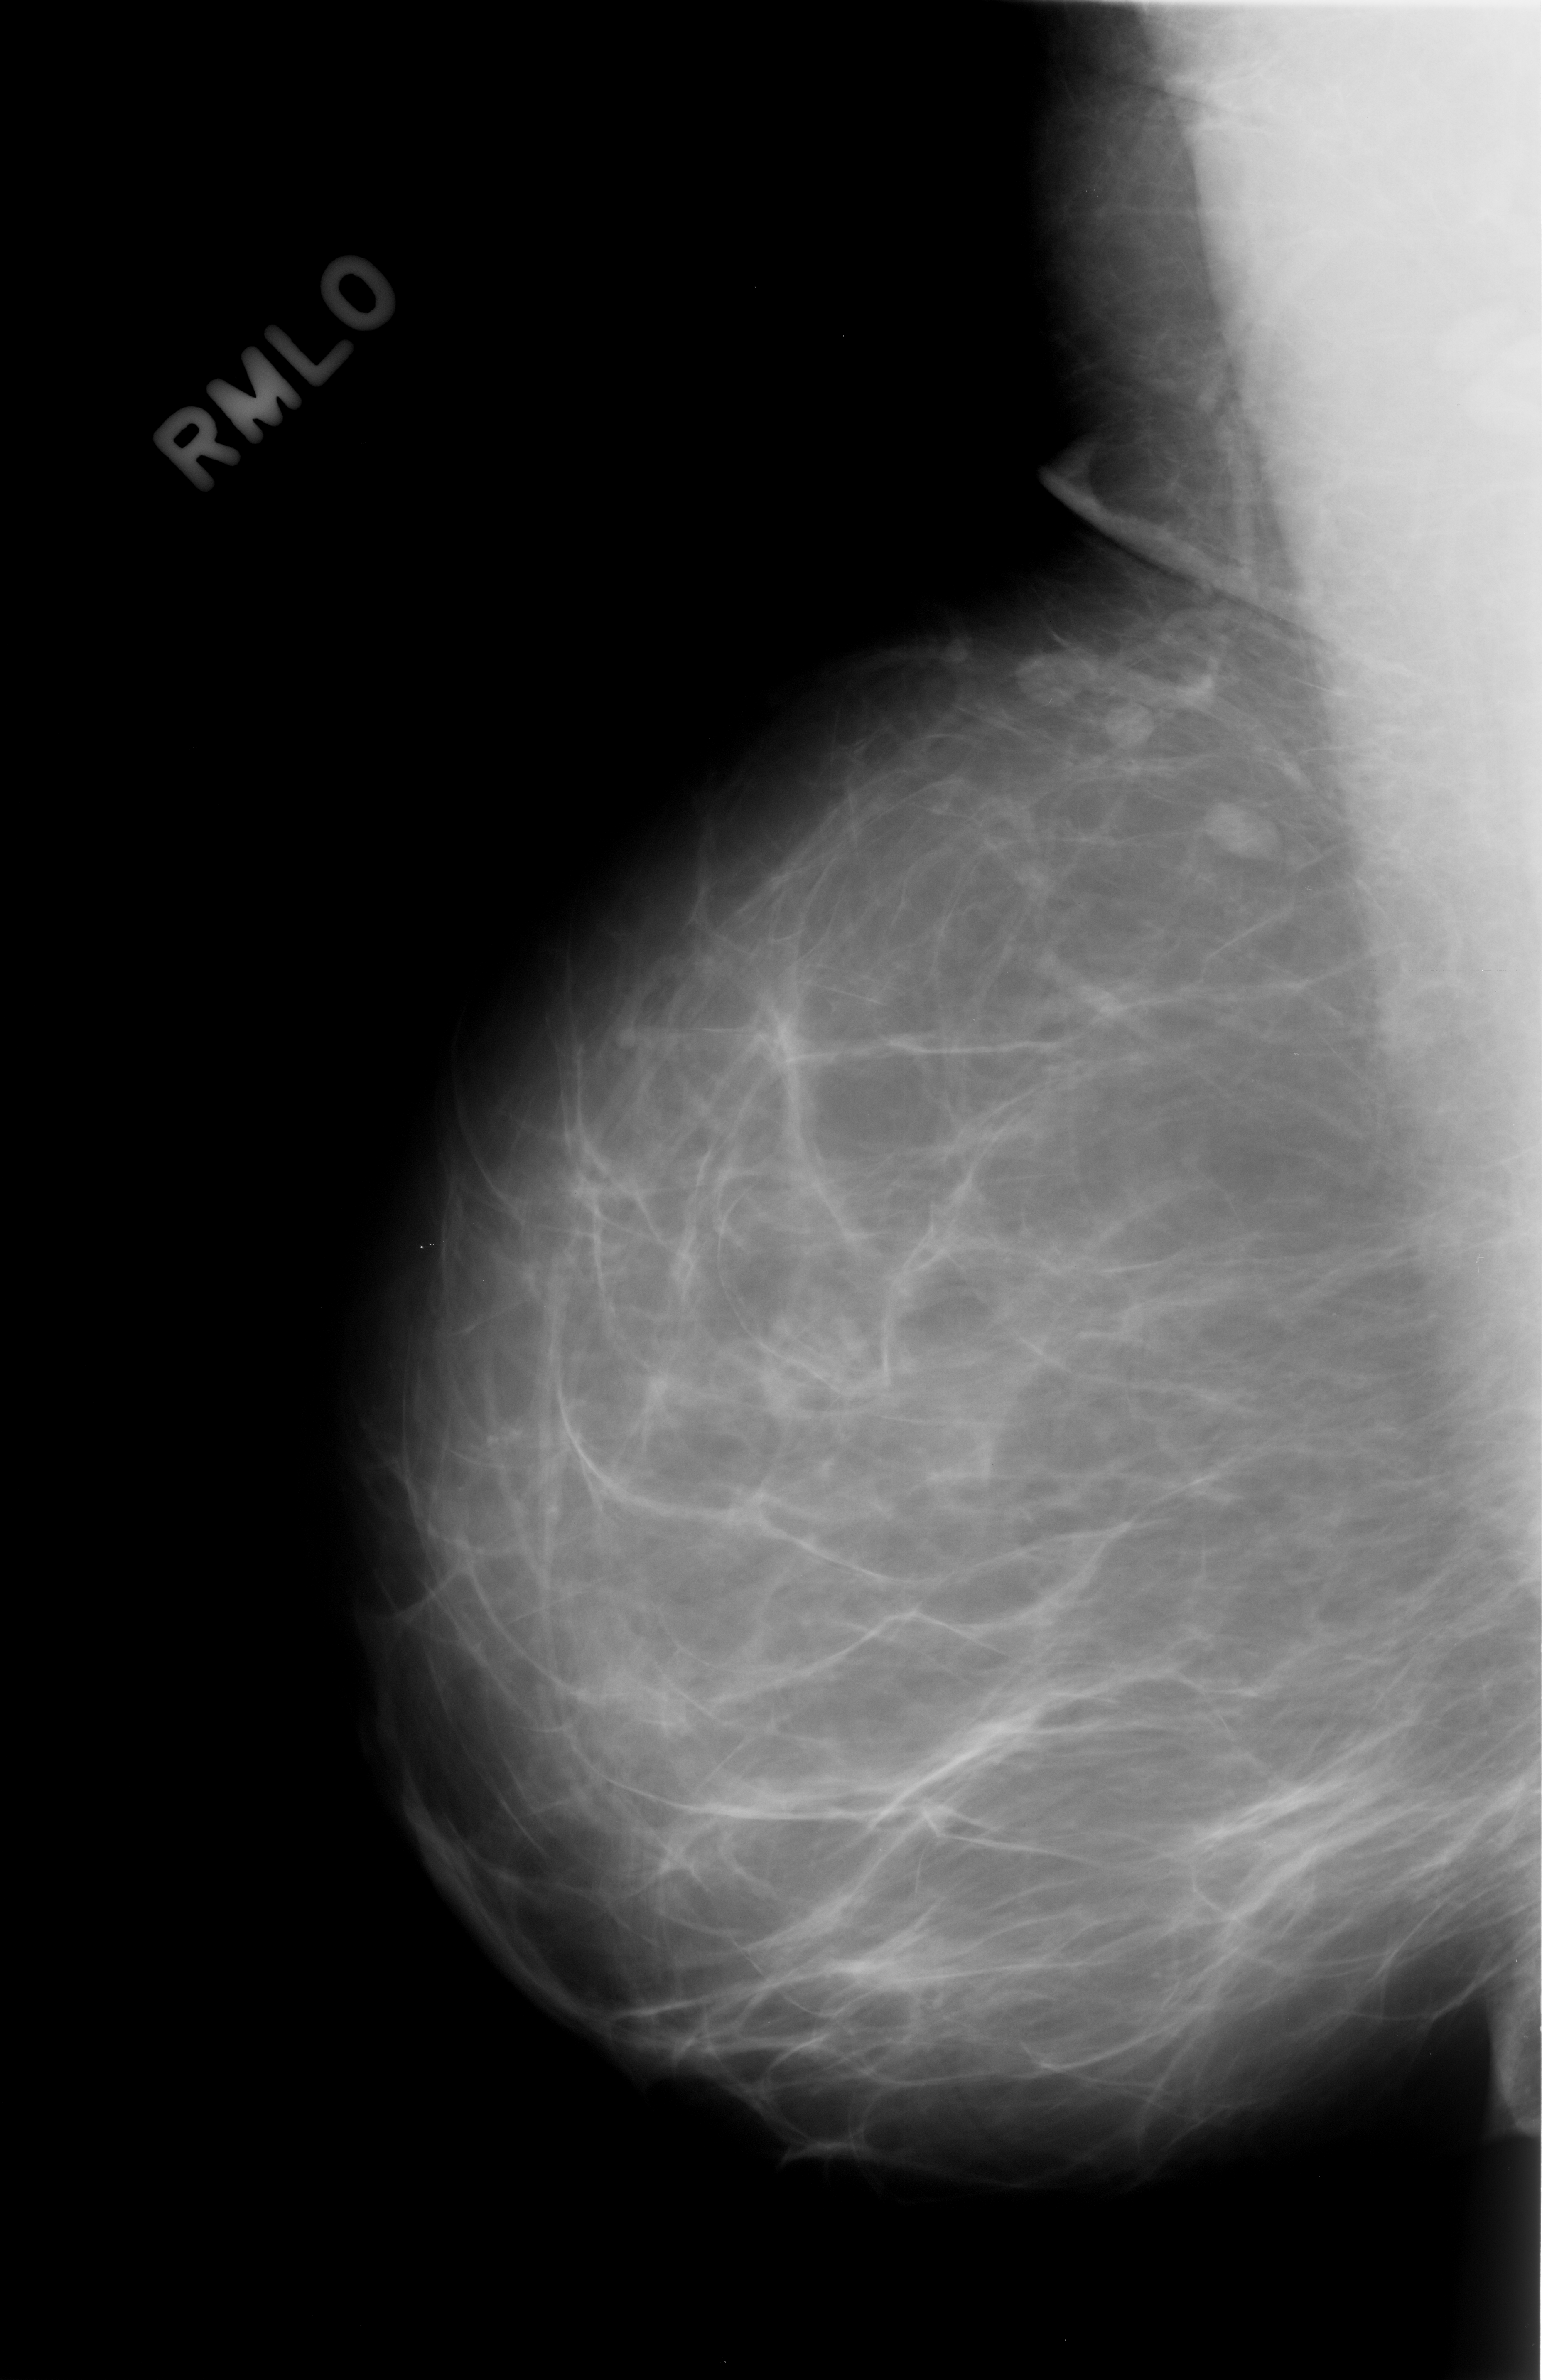
Scanned film-screen mammogram. Right breast. Mediolateral oblique (MLO) view. 1542 × 2380 image matrix.
Expert-marked regions of interest on this film, with their recorded descriptors:
- Finding 1 of 3: mass, shape lobulated, margins circumscribed; BI-RADS assessment category 3; outcome (as recorded, no biopsy): benign without callback (not worked up further): bounding box [x1, y1, x2, y2] px = [1013, 644, 1097, 714]
- Finding 2 of 3: mass, shape round, margins circumscribed; BI-RADS assessment category 3; subtlety rating 5 on a 1 (subtle) to 5 (obvious) scale; outcome (as recorded, no biopsy): benign without callback (not worked up further): [1078, 690, 1162, 760]
- Finding 3 of 3: mass, shape oval, margins circumscribed; BI-RADS assessment category 3; subtlety rating 5 on a 1 (subtle) to 5 (obvious) scale; benign; no additional work-up was recommended (outcome (as recorded, no biopsy): benign without callback): [1191, 794, 1280, 861]